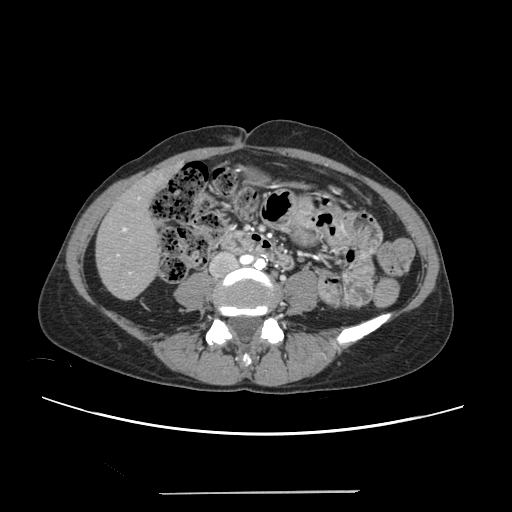
Contrast-enhanced abdominal CT, one axial slice. Slice 49 of 240 in the series (ordered by position). 120 kVp. Intravenous contrast given. Soft-tissue window (W 400 / L 40 HU). 512 × 512 image matrix, field of view 371 × 371 mm. Female patient, age 60 years. From the clinical record (not read from this slice): diagnosis: colorectal cancer liver metastases, imaged before liver resection; multiple liver metastases: no; largest metastasis: 1.5 cm; disease in both lobes: no.
Annotated regions visible in this slice (manually delineated by an expert):
- liver: bounding box [x1, y1, x2, y2] px = [97, 169, 174, 299]
- planned liver remnant (the part of the liver to remain after resection): [97, 171, 169, 299]
- portal vein (with intrahepatic branches): [116, 196, 140, 274]